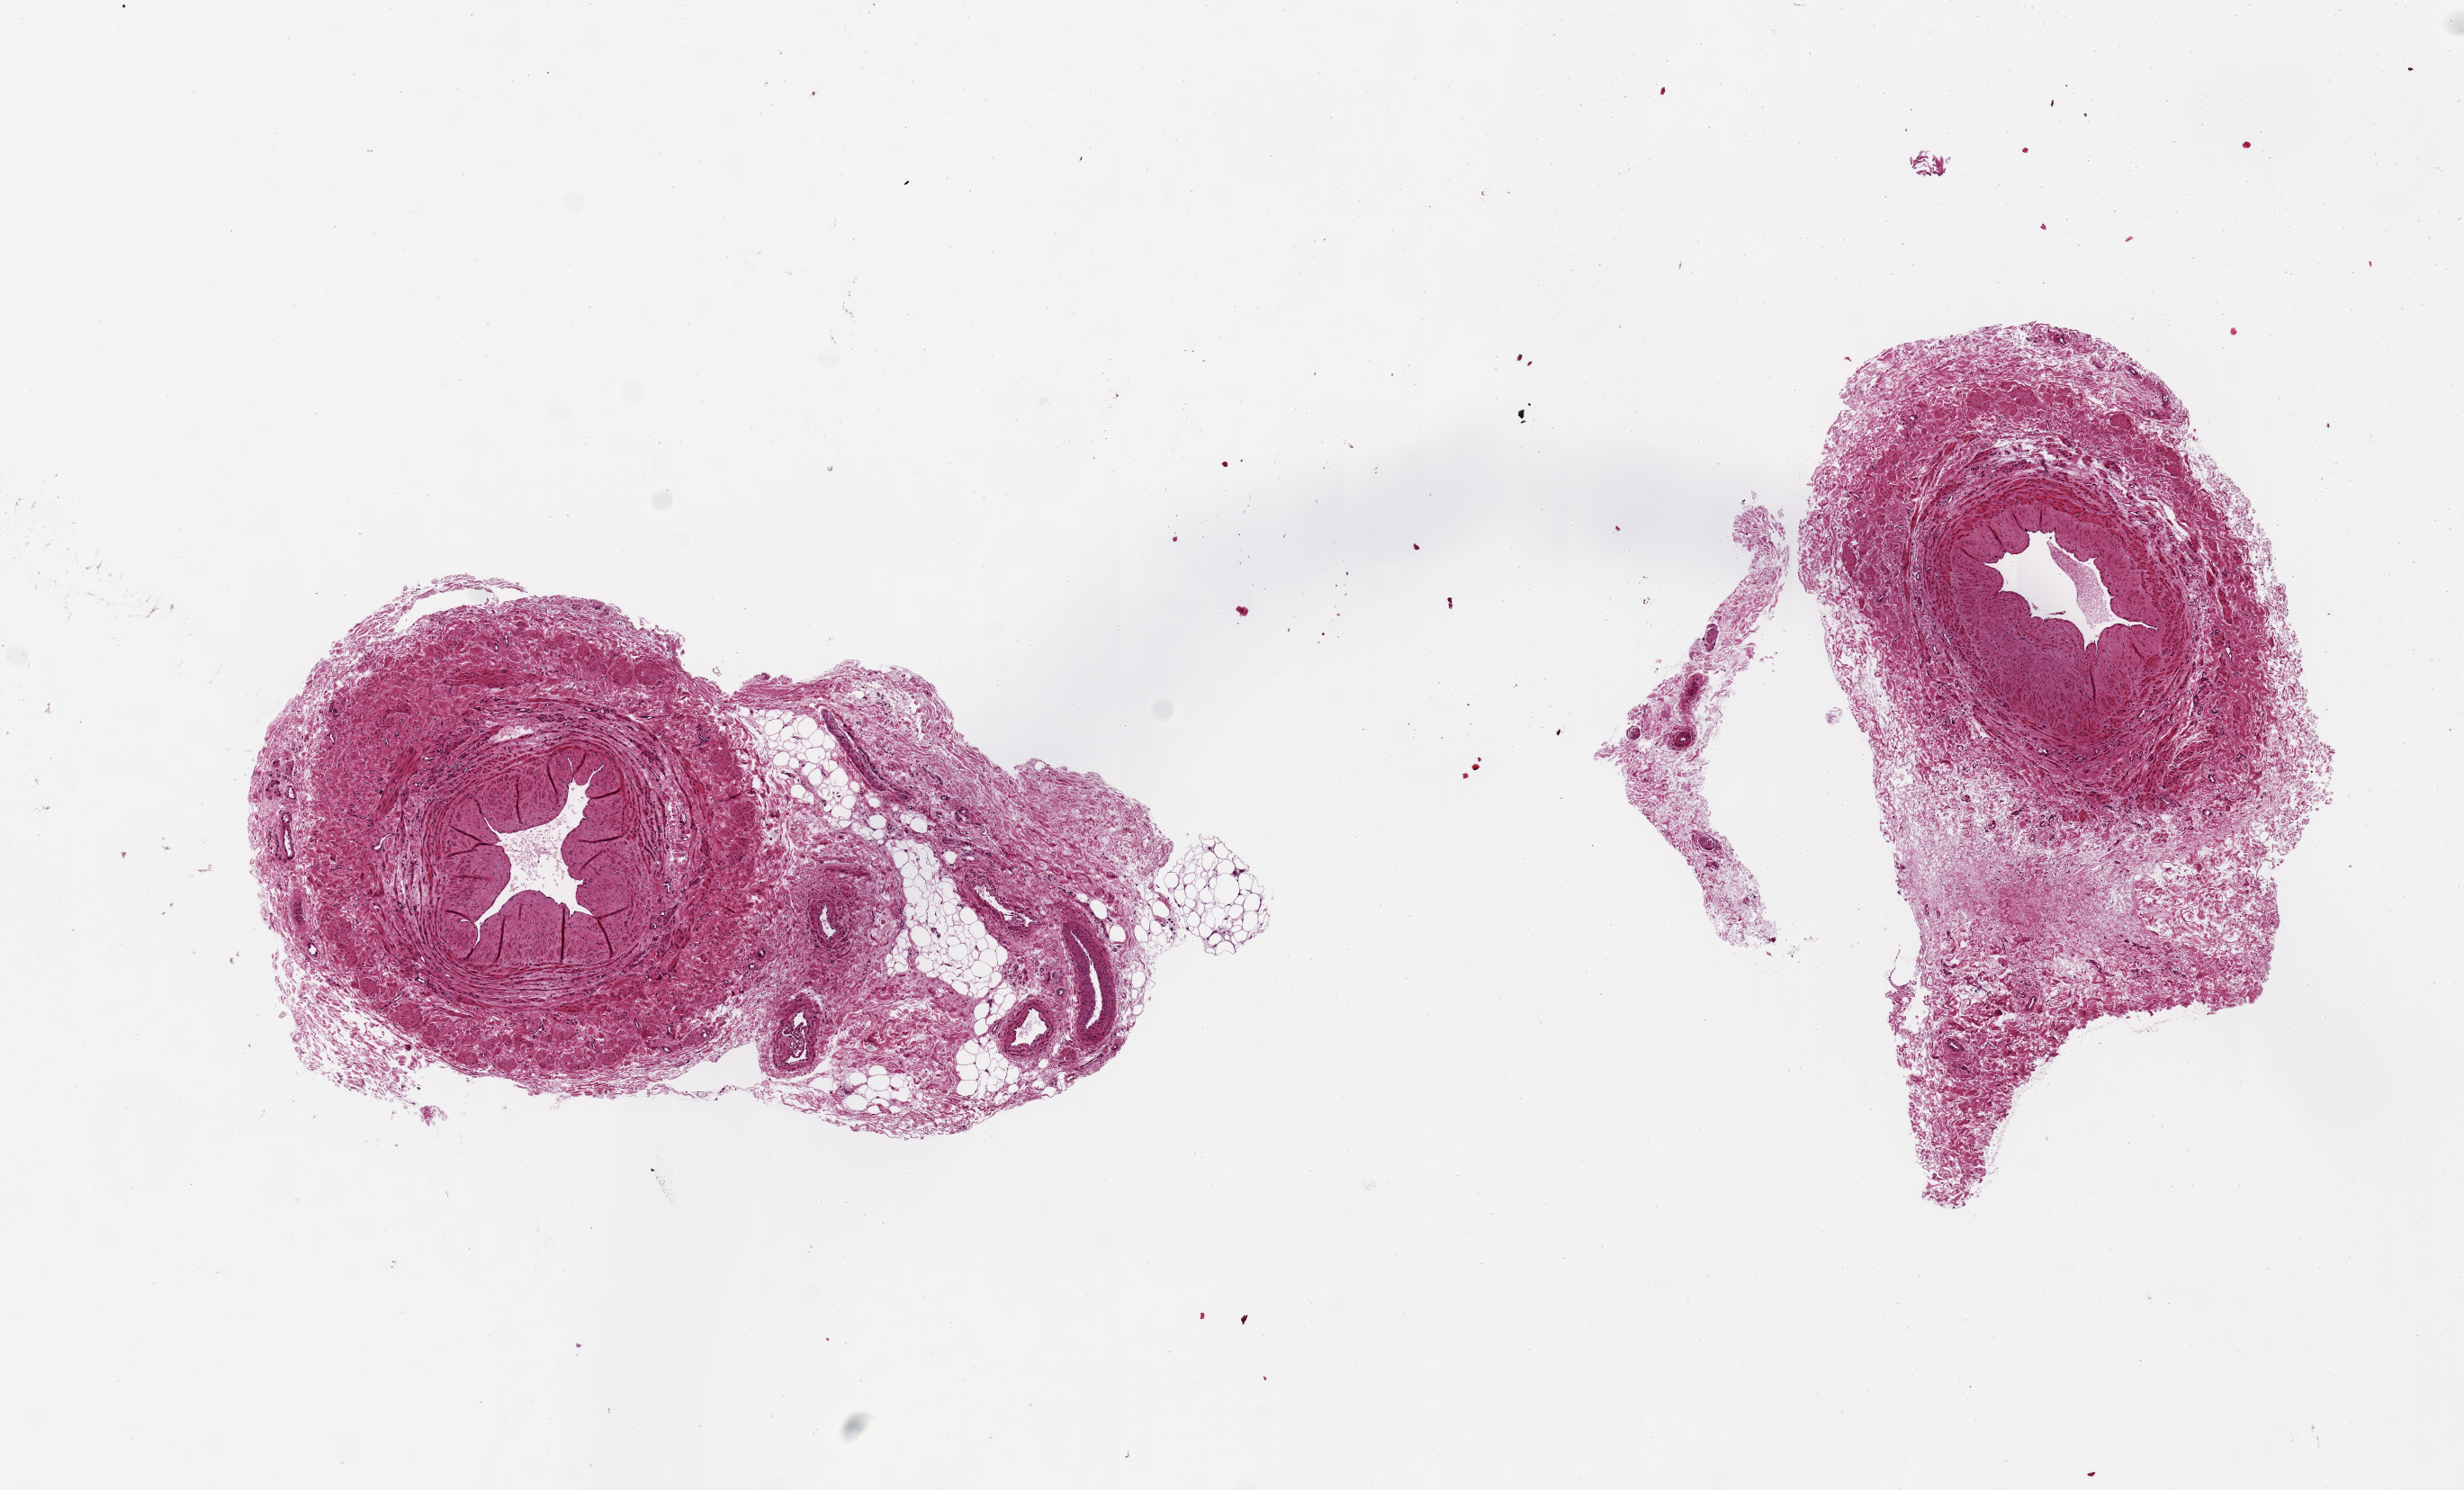
Digitized haematoxylin and eosin-stained section, brightfield, shown as a low-resolution overview of the whole scanned area (about 10.8 x 6.5 mm), PAXgene-fixed paraffin-embedded (PFPE) section, section of tibial artery (target tissue), donor tissue sample.
Review note (as recorded): 2 ~4x2mm aliquots. ~50% of aliquots are peri-arterial connective tissue, fat, small vessels.